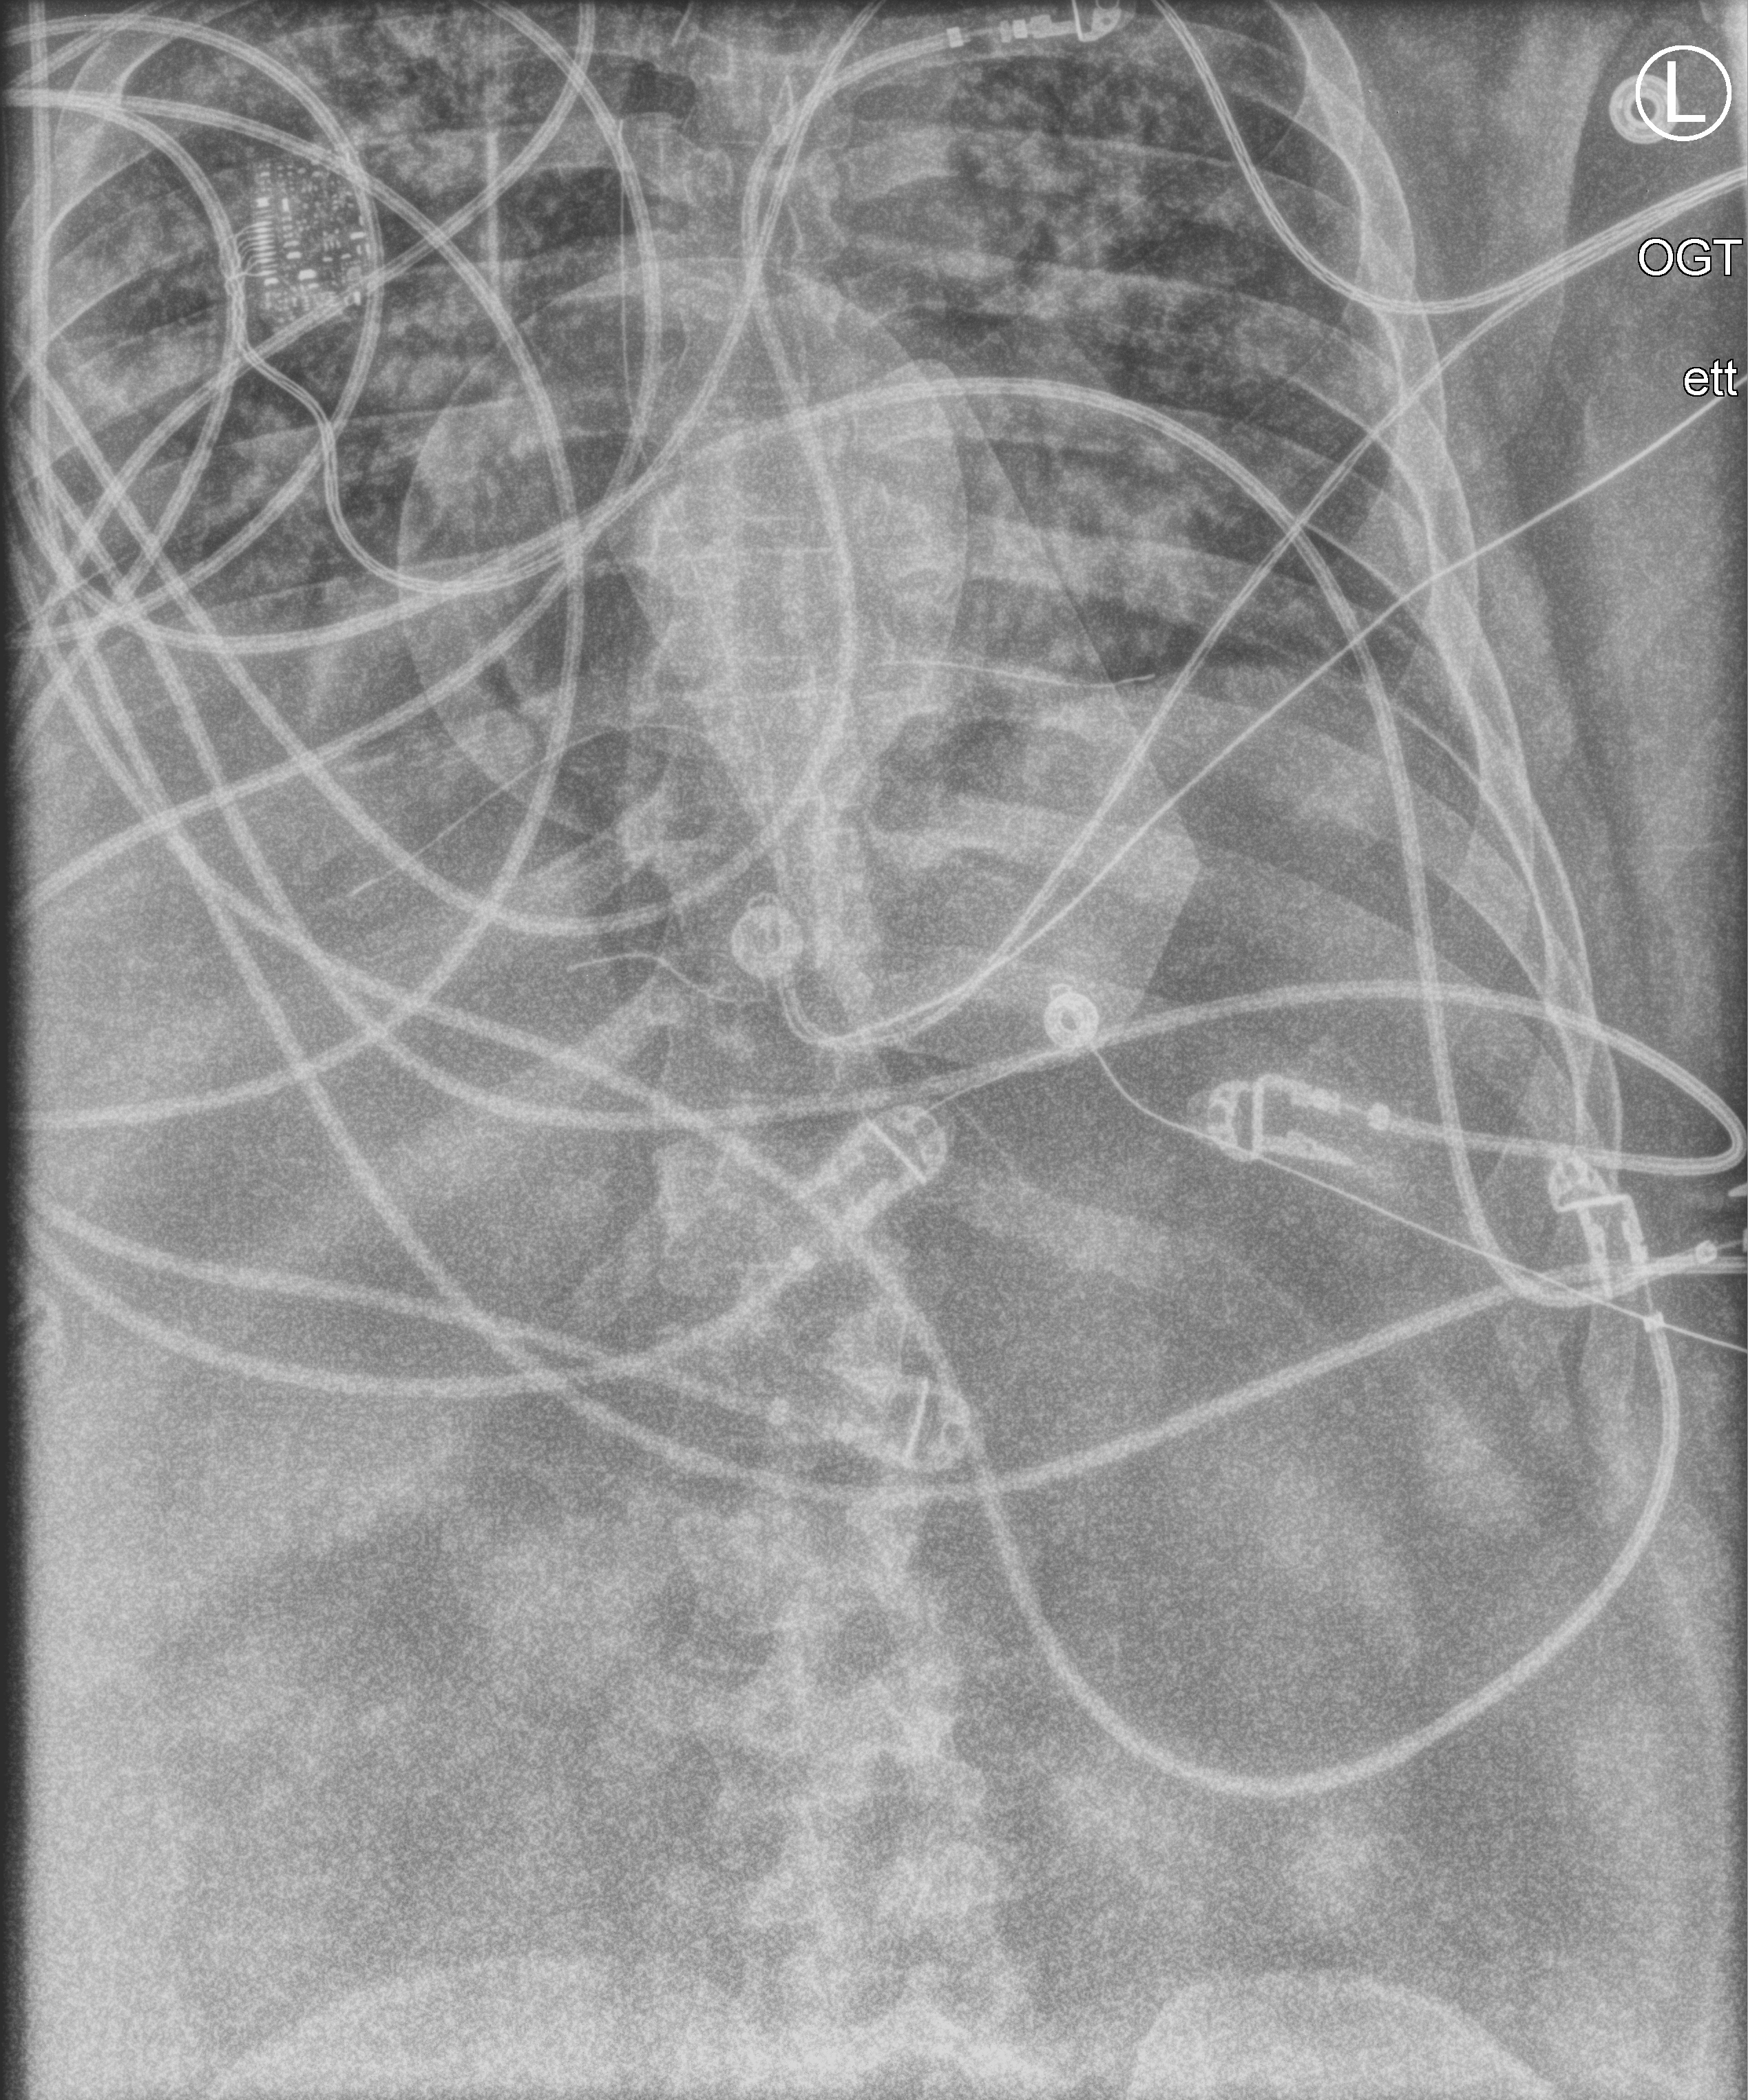
Portable chest radiograph; anteroposterior (AP) projection. Adult patient hospitalised with COVID-19, age 18–59 years.
Admission-level facts for this patient (not findings on this image; timing relative to this image not recorded):
- hypertension (admission record): no